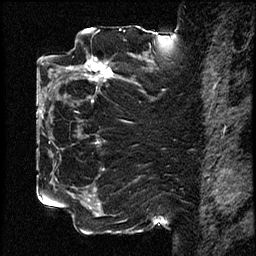
Breast MRI (dynamic contrast-enhanced), one sagittal slice. Slice 41 of 78 in the series (ordered by position). Dynamic contrast-enhanced study with each time point stored as its own series, time point 2 of 3 at this slice position (early post-contrast, ordered by acquisition time). 1.5 T. TE 4.2 ms, TR 17.6 ms. 2 mm slice thickness. 256 × 256 image matrix, field of view 200 × 200 mm. Female patient, age 42 years. From the clinical record (not read from this slice): setting: breast cancer imaged before/during neoadjuvant chemotherapy; receptor status: HER2-positive.
Outlined on this slice (semi-automatic segmentation, software-assisted and operator-edited):
- analysis volume of interest (the breast-tissue region the enhancement analysis was run in; not a lesion): bounding box [x1, y1, x2, y2] px = [50, 48, 131, 123]
- tumour enhancement mask (voxels above the 100 % enhancement threshold inside the analysis volume of interest): [84, 60, 113, 82]